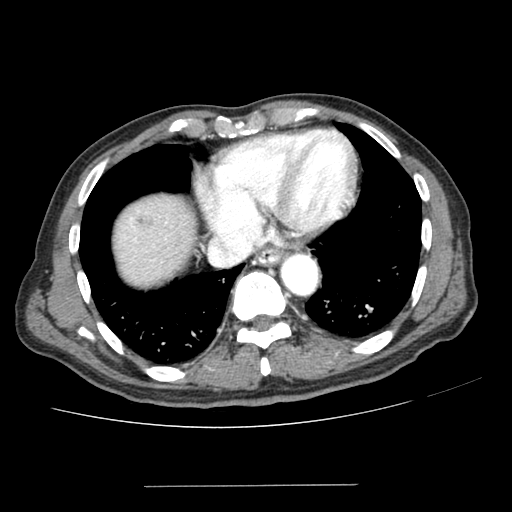
Contrast-enhanced abdominal CT (liver protocol), one axial slice. Position 179 of 187 along the scan axis. 100 kVp. Soft-tissue window (W 400 / L 40 HU). 2.5 mm slice thickness. 512 × 512 image matrix, field of view 360 × 360 mm. From the clinical record (not read from this slice): diagnosis: hepatocellular carcinoma (patient treated with transarterial chemoembolisation; whether this scan precedes or follows treatment is not stated here); TNM stage (as recorded): Stage-I; Child-Pugh class: A; tumour nodularity: uninodular; tumour size: 1.6 cm.
Outlined on this slice (semi-automatically segmented with operator editing):
- abdominal aorta: bounding box (x1, y1, x2, y2) in pixels: (281, 254, 318, 294)
- liver parenchyma outside the tumour (the mass and vessels are separate outlines, so this box may not span the whole liver): (114, 194, 196, 284)
- mass: (137, 212, 153, 232)